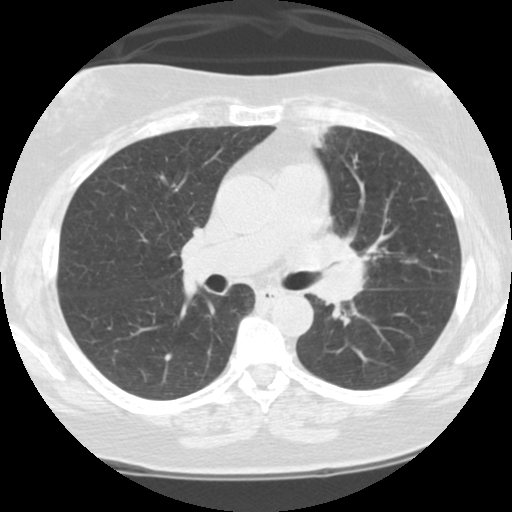
Low-dose screening chest CT, one axial slice. Position 64 of 108 along the scan axis. Reconstruction kernel STANDARD. Lung window (W 1500 / L -600 HU). 2.5 mm slice thickness. 512 × 512 image matrix, field of view 300 × 300 mm.
Structures marked on this image (outlined manually by an expert reader):
- lesion 1 (tumor, hilum of left lung): bounding box [x1, y1, x2, y2] px = [304, 237, 365, 312]